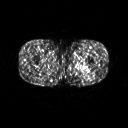
FDG PET of an extremity soft-tissue mass (from a PET/CT study), one axial slice; slice 238 of 267 in the series (ordered by position); 128 × 128 image matrix, field of view 500 × 500 mm. Male patient, age 27 years. From the clinical record (not read from this slice): histological type: extraskeletal osteosarcoma; grade: high; site of the primary tumour: left adductur.
Structures marked on this image (expert contour drawn on MRI and transferred to this co-registered scan by the dataset authors):
- gross tumour volume (mass): bounding box [x1, y1, x2, y2] px = [69, 61, 95, 74]